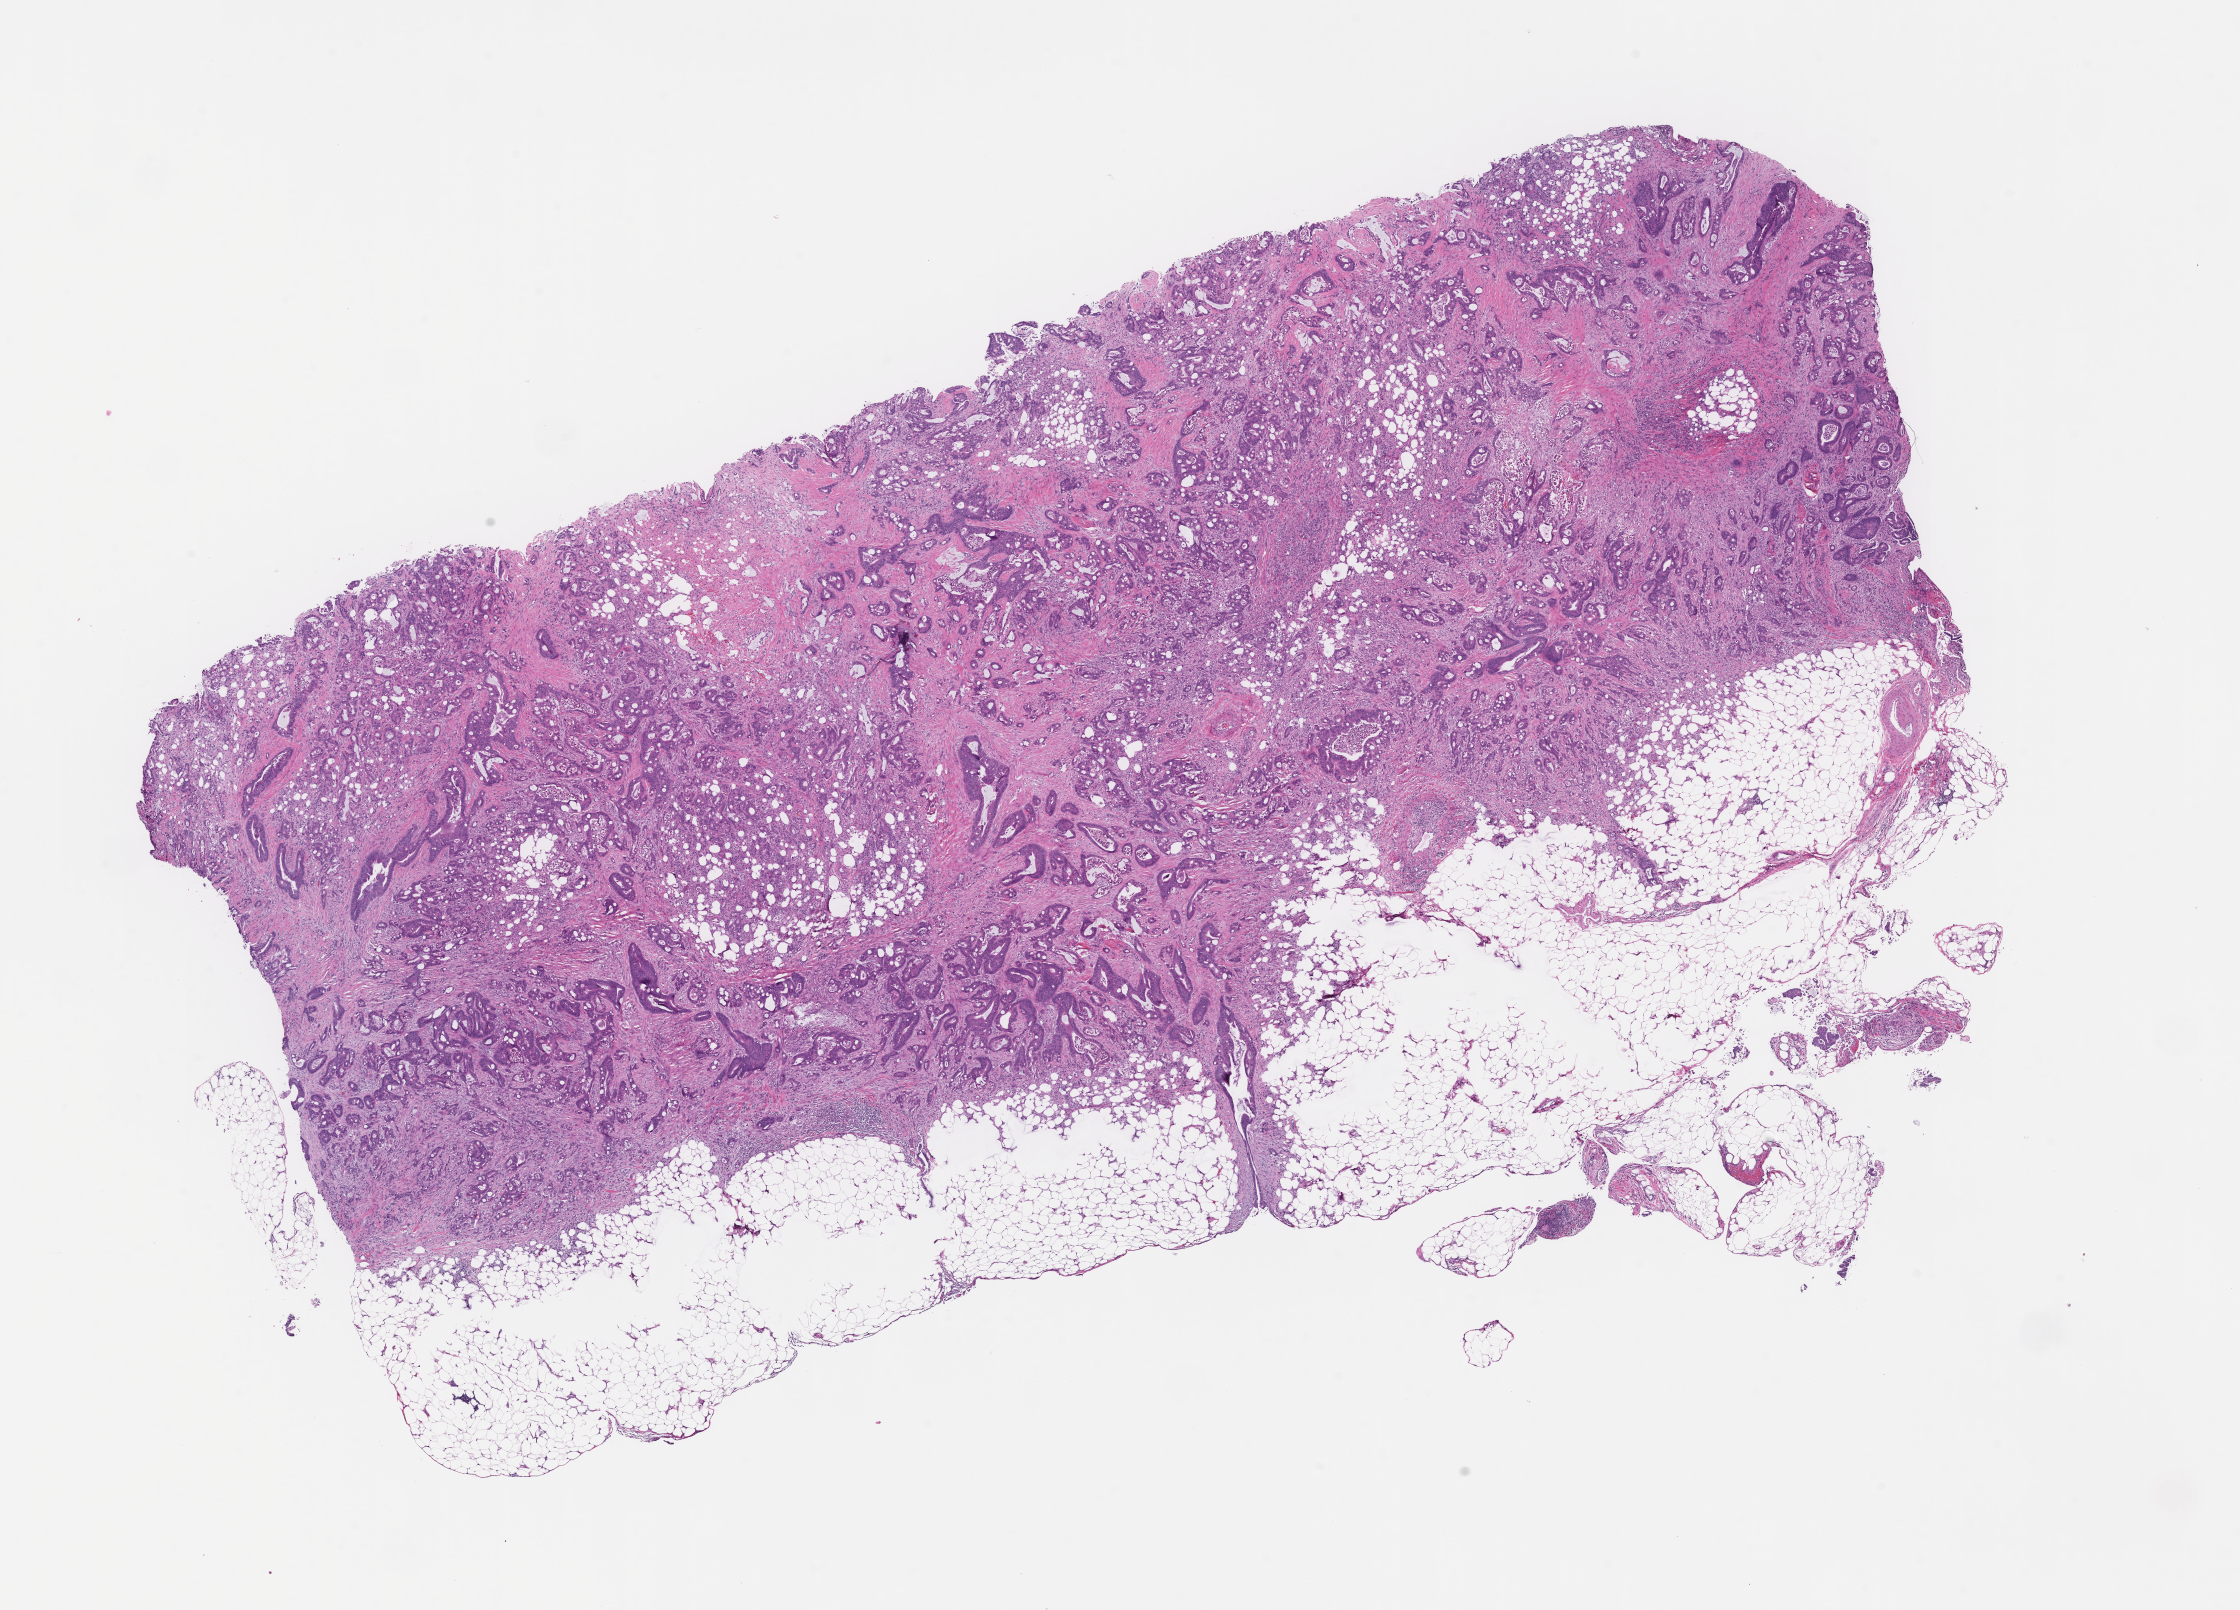
Haematoxylin and eosin whole-slide image, low-resolution overview of the scanned area, about 18.1 x 13.0 mm. Formalin-fixed paraffin-embedded section. Female patient.
This section: metastasis (sampled organ not recorded). Primary diagnosis of the patient: Colorectal Carcinoma.